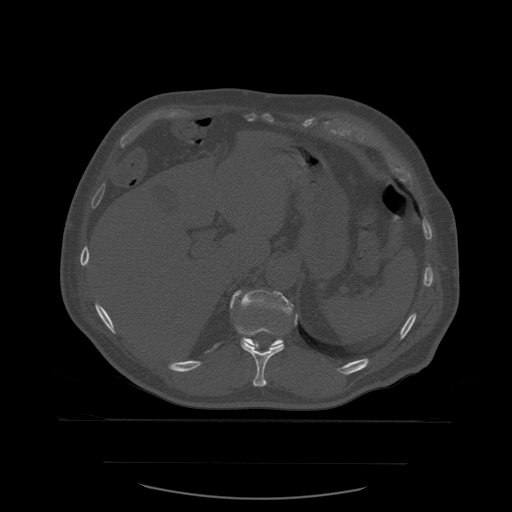
CT including the spine, one axial slice; slice 288 of 590 in the series (ordered by position); bone window (W 1800 / L 400 HU); 512 × 512 image matrix, field of view 479 × 479 mm. Patient age 71 years. From the clinical record (not read from this slice): primary cancer: lung.
Annotated regions visible in this slice (semi-automatically segmented with operator editing):
- T11 vertebra: box from (x=236, y=315) to (x=298, y=387) px
- T12 vertebra: (x=230, y=290)–(x=299, y=352)